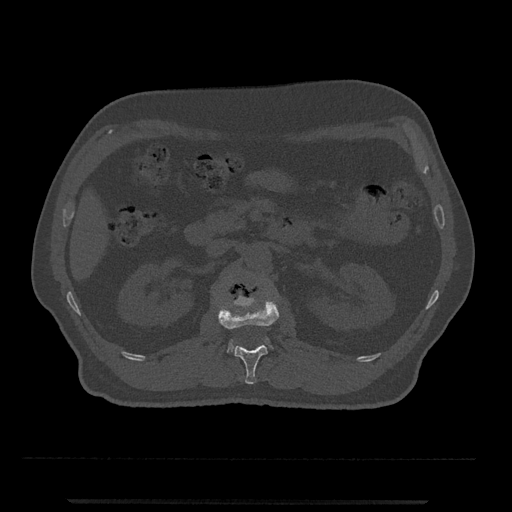
CT including the spine, one axial slice. Position 311 of 797 along the scan axis. Reconstruction kernel Br40s/3. 120 kVp. Bone window (W 1800 / L 400 HU). 0.5 mm slice thickness. 512 × 512 image matrix, field of view 419 × 419 mm. Male patient, age 63 years. Case-level facts recorded for this patient, not image findings: primary cancer: prostate.
Outlined on this slice (semi-automatically segmented with operator editing):
- L1 vertebra: bounding box [x1, y1, x2, y2] px = [218, 292, 279, 384]
- L2 vertebra: [227, 274, 273, 353]